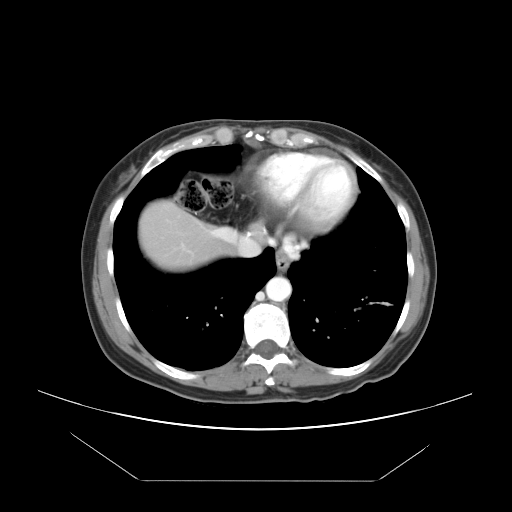
Contrast-enhanced abdominal CT, one axial slice. Position 41 of 45 along the scan axis. Reconstruction kernel STANDARD. 120 kVp. Intravenous contrast given. Soft-tissue window (W 400 / L 40 HU). 5 mm slice thickness. 512 × 512 image matrix. Female patient, age 52 years. Case-level facts recorded for this patient, not image findings: diagnosis: colorectal cancer liver metastases, imaged before liver resection; multiple liver metastases: yes; largest metastasis: 2.5 cm; chemotherapy before resection: yes.
Structures marked on this image (outlined manually by an expert reader):
- hepatic veins: bounding box (x1, y1, x2, y2) in pixels: (181, 229, 256, 256)
- liver: (142, 205, 231, 270)
- planned liver remnant (the part of the liver to remain after resection): (142, 205, 231, 270)